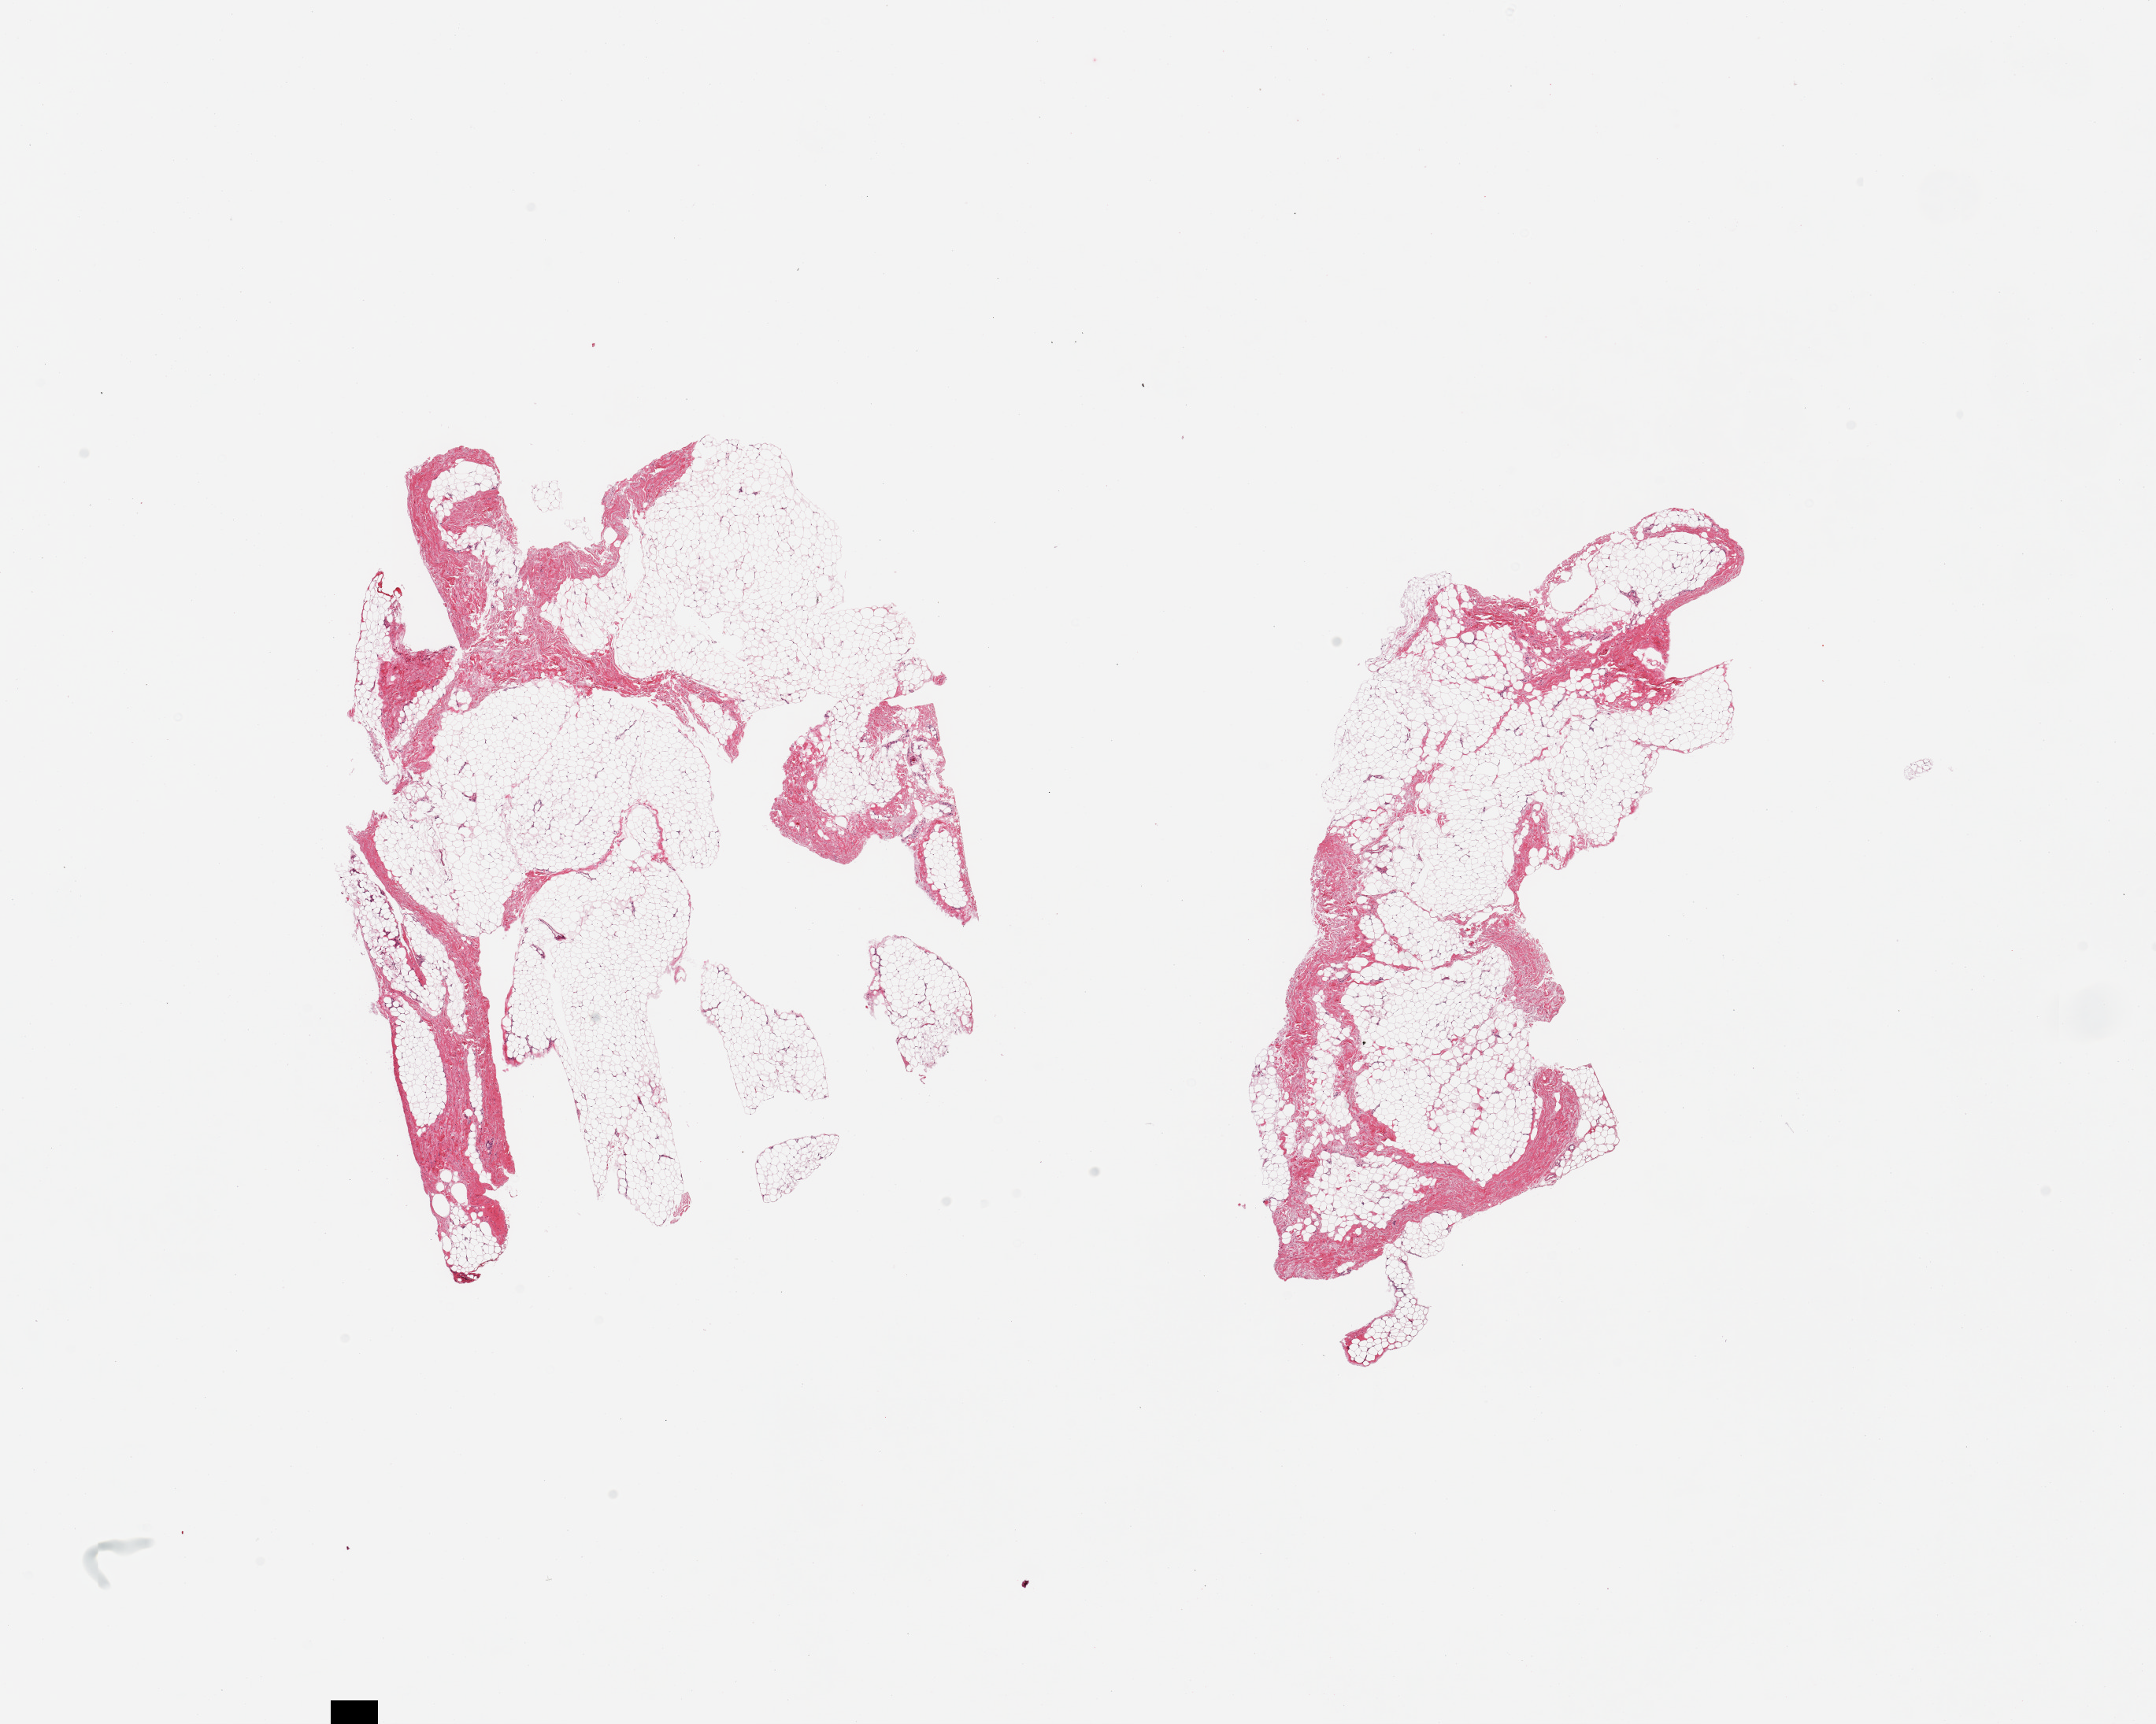
Digitized hematoxylin and eosin (H&E)-stained section, brightfield, shown as a low-resolution overview of the whole scanned area (about 21.7 x 17.3 mm, from a 20x scan), PAXgene-fixed paraffin-embedded (PFPE) section, section of breast (target tissue), tissue donor sample. Male donor.
Review note (as recorded): 2 pieces, fibroadipose elements only; no ductal elements noted.